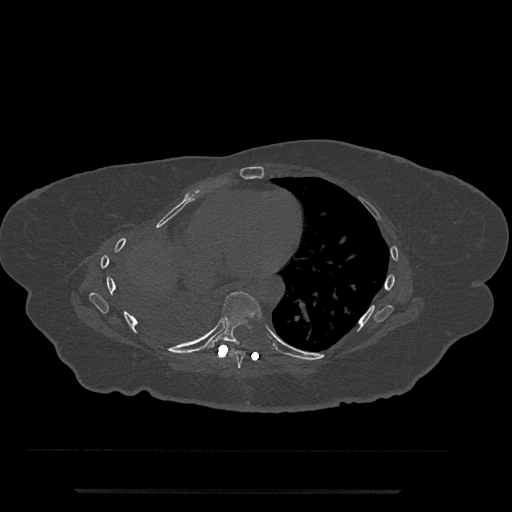
CT including the spine, one axial slice. Position 410 of 797 along the scan axis. Bone window (W 1800 / L 400 HU). 0.5 mm slice thickness. 512 × 512 image matrix, field of view 440 × 440 mm. Female patient, age 51 years. From the clinical record (not read from this slice): primary cancer: neuro; vertebrae with lytic lesions (as recorded): T8.
Outlined on this slice (semi-automatic segmentation, software-assisted and operator-edited):
- T7 vertebra: bounding box (x1, y1, x2, y2) in pixels: (229, 349, 245, 369)
- T8 vertebra: (207, 291, 262, 349)